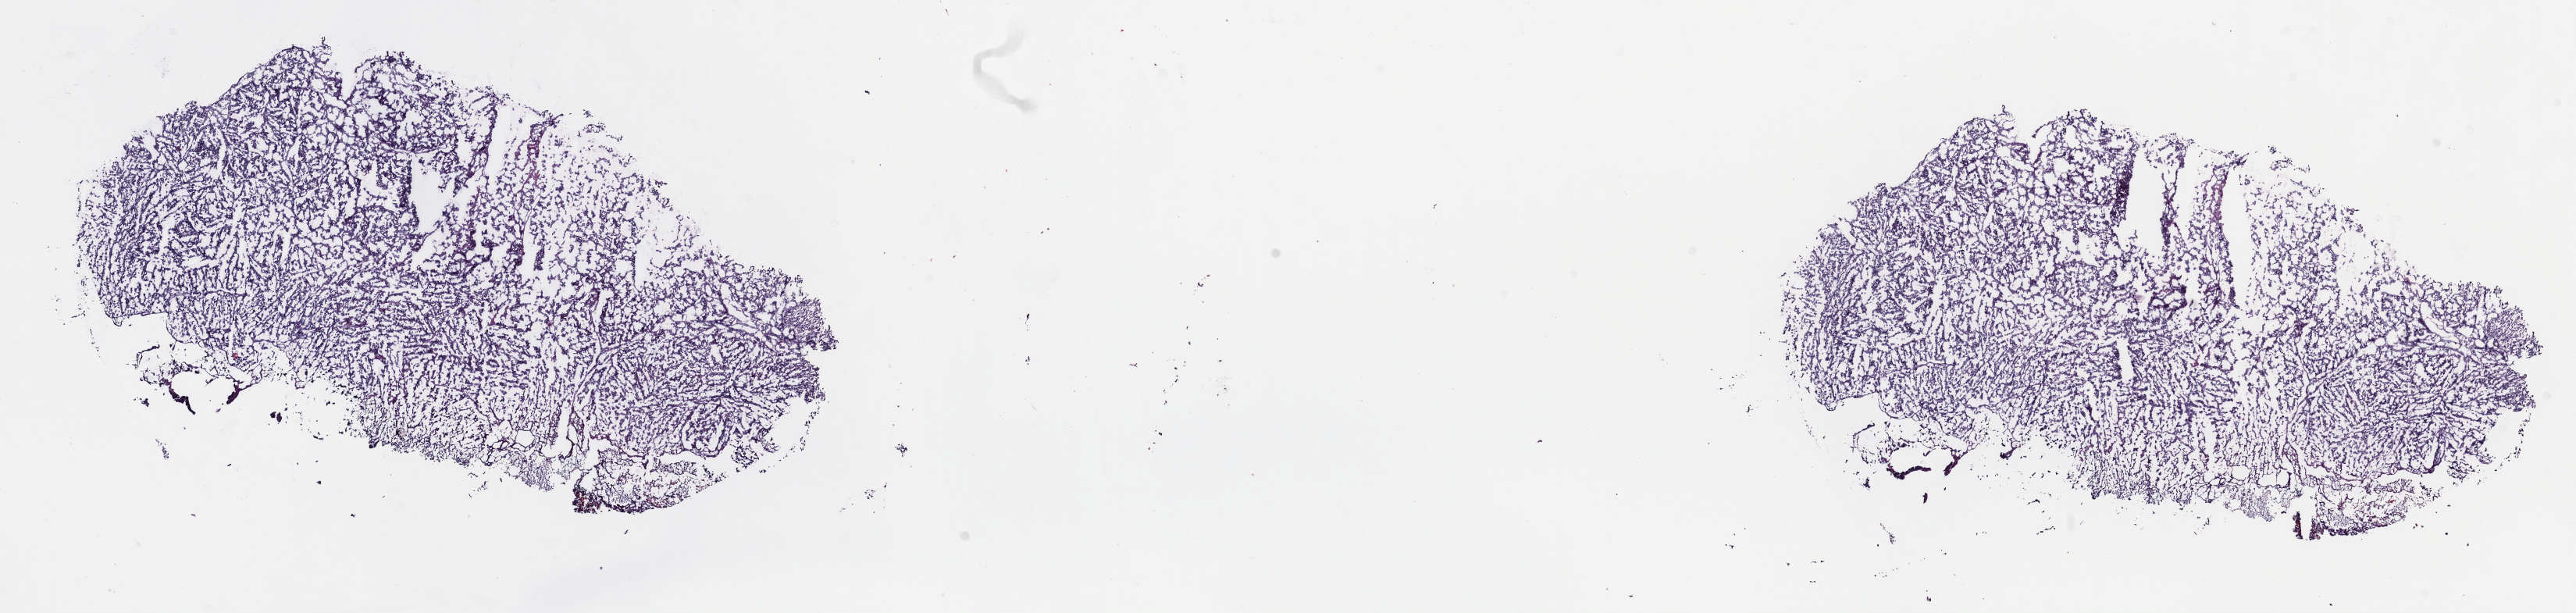
H&E whole-slide image — low-resolution overview of the scanned area, about 26.7 x 6.3 mm (from a 40x scan); frozen section; sample: primary tumour, bladder. Female, age 75 years at initial diagnosis. Pathologist review of this section (percent, as recorded): tumour cells 100%, tumour nuclei 80%.
Pathologic diagnosis: Transitional cell carcinoma.